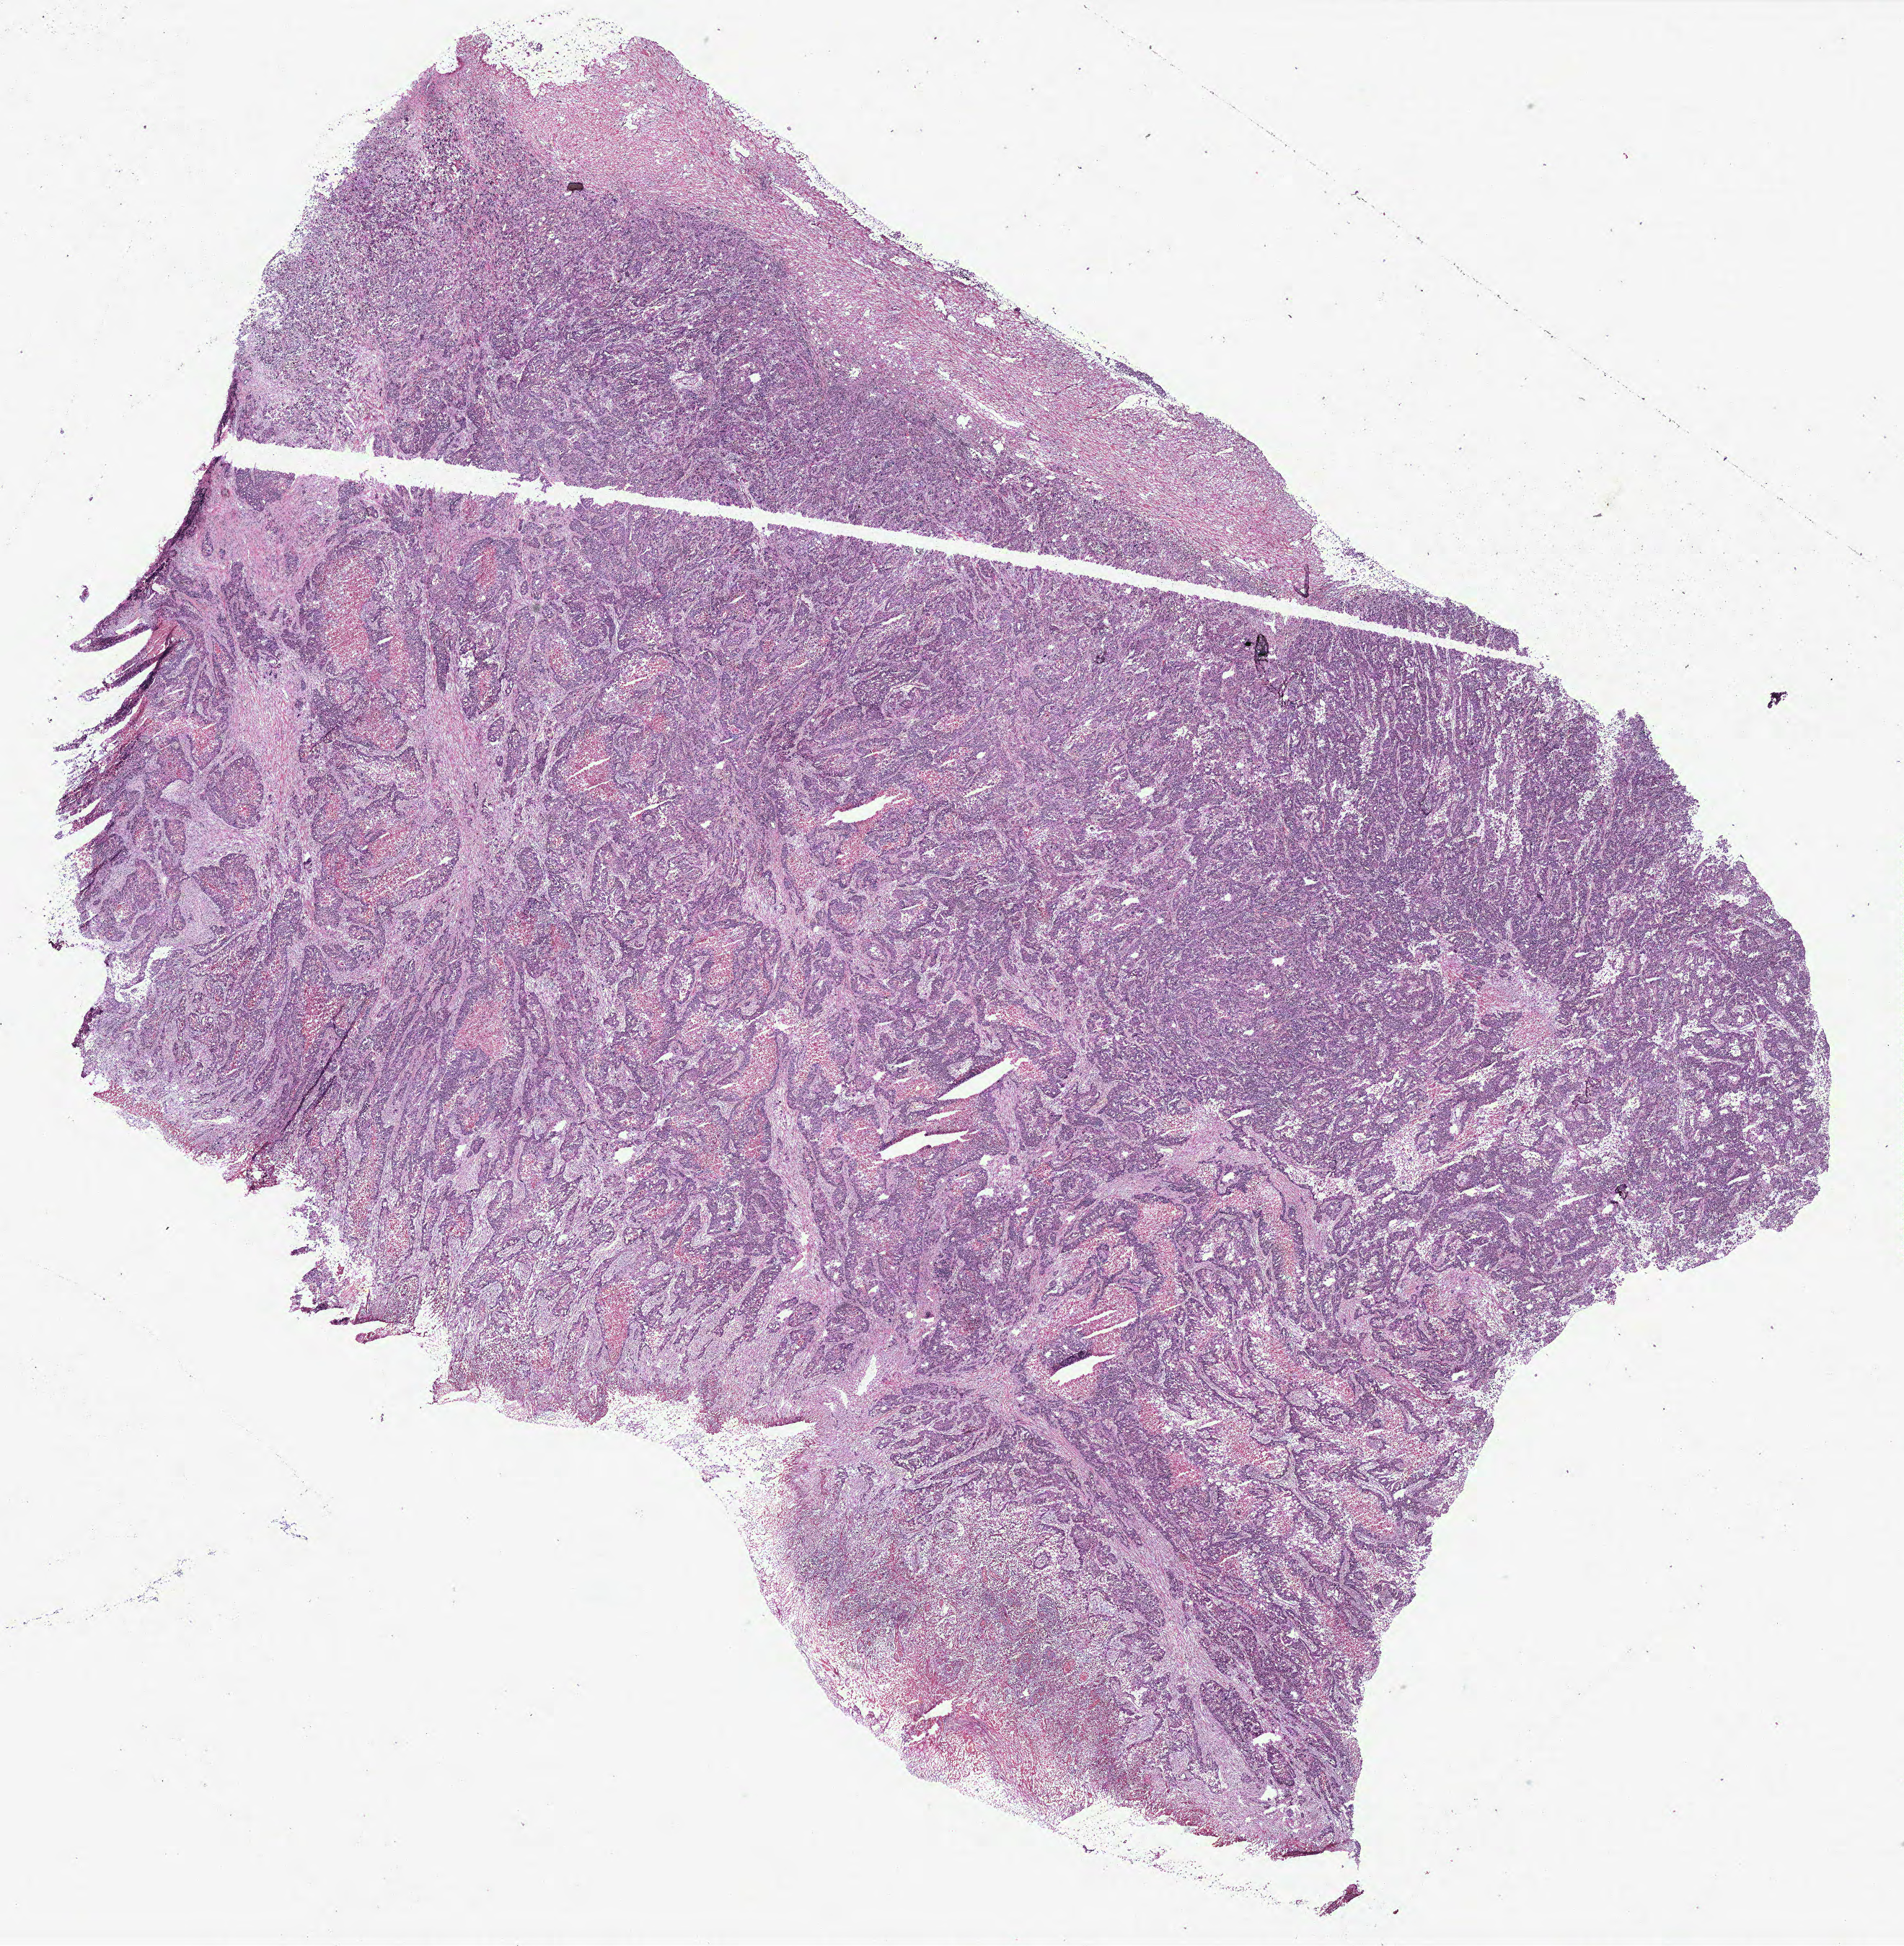
H&E whole-slide image, shown as a low-resolution overview of the whole scanned area (about 21.1 x 21.6 mm); colon, tissue type not recorded.
* patient diagnosis (cohort enrolment): colon cancer (colon)